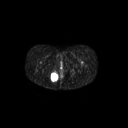
FDG PET of an extremity soft-tissue mass (from a PET/CT study), one axial slice. Position 29 of 267 along the scan axis. 3.27 mm slice thickness. 128 × 128 image matrix, field of view 700 × 700 mm. Female patient, age 17 years. From the clinical record (not read from this slice): histological type: epithelioid sarcoma; grade: intermediate; site of the primary tumour: right buttock.
Outlined on this slice (expert contour drawn on MRI and transferred to this co-registered scan by the dataset authors):
- gross tumour volume including surrounding oedema: bounding box [x1, y1, x2, y2] px = [49, 71, 59, 83]
- gross tumour volume (mass): [50, 72, 59, 81]